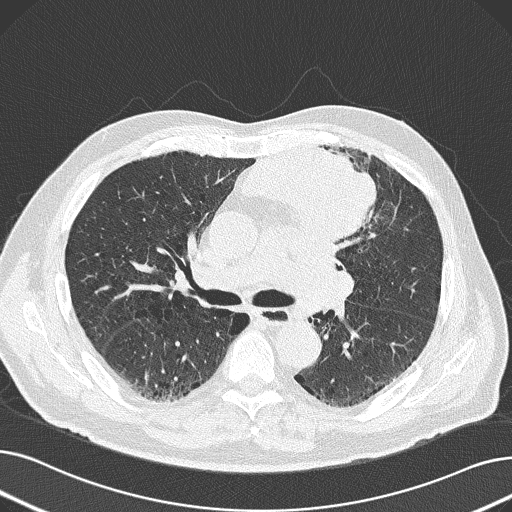
Axial slice from a low-dose chest CT screening exam; first (baseline) screen; lung window (W 1500 / L -600 HU); 2 mm slice thickness; slice 74 of 165 in the series. Male, age 69 years at enrolment. Former smoker at enrolment.
Expert reader's lesion annotation, box from (x=235, y=134) to (x=384, y=250) px. Screening reader's record for this exam (one nodule recorded; not confirmed to be the boxed lesion): non-calcified nodule or mass ≥4 mm, left upper lobe, 6 × 10 mm, spiculated (stellate) margins, soft tissue attenuation. Official screen result: positive, change unspecified: nodule(s) >= 4 mm or enlarging nodule(s), mass(es), or other non-specific abnormalities suspicious for lung cancer. Later outcome: lung cancer diagnosed 20 days after this screen — non-small cell carcinoma, left upper lobe, poorly differentiated (G3), stage IB (AJCC 6th edition), 100 mm at pathology.